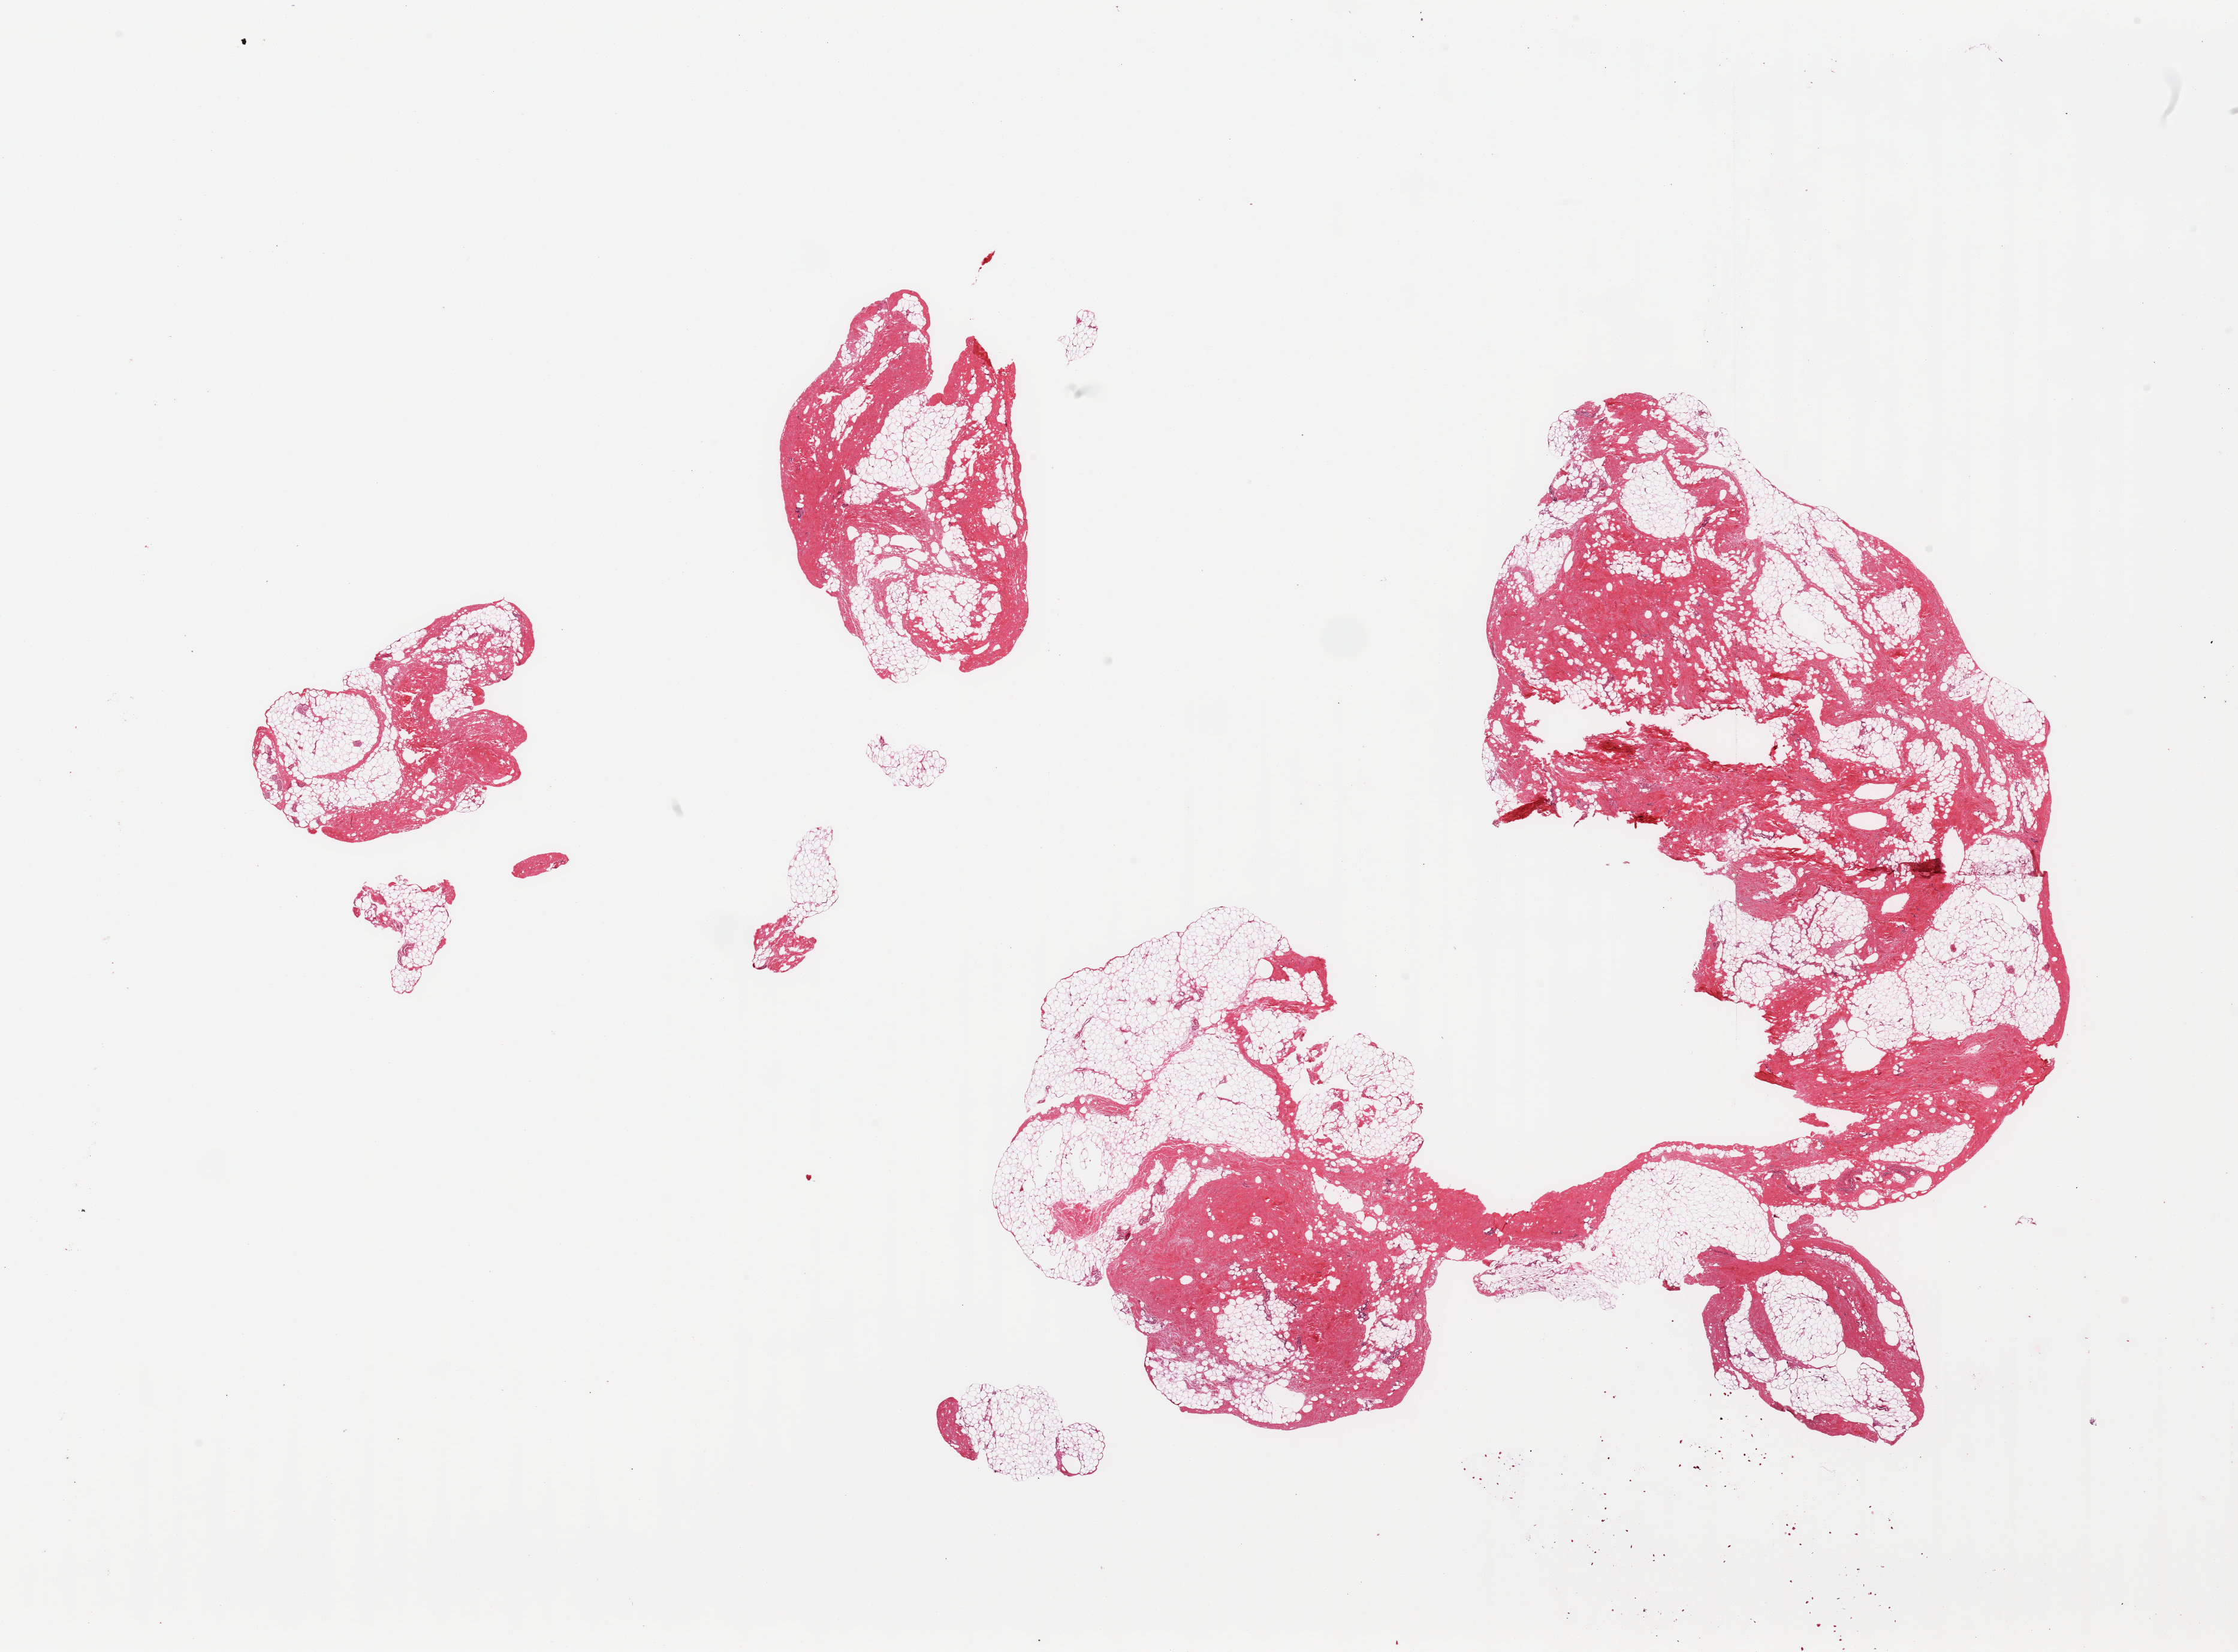
Digitized hematoxylin and eosin (H&E)-stained section, brightfield — low-resolution overview of the scanned area, about 29.5 x 21.8 mm; PAXgene-fixed, paraffin-embedded tissue; sampled site (target tissue): breast; tissue donor sample. Male donor.
Pathologist's review note for this sample: 3 fragmented pieces of fibroadipose tissue without mammary ducts.